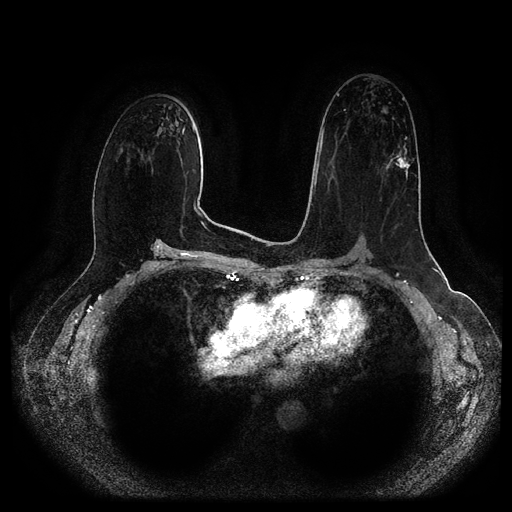
Breast MRI (dynamic contrast-enhanced, multi-phase), one axial slice; position 60 of 116 along the scan axis; dynamic contrast-enhanced series, time point 2 of 5 at this slice position (early post-contrast); 1.5 T; TE 2.6 ms, TR 5.2 ms; 512 × 512 image matrix, field of view 380 × 380 mm. Female patient, age 57 years.
Structures marked on this image (semi-automatically segmented with operator editing):
- breast lesion (labelled 'tumour' in the annotation; benign lesions carry a separate 'benign' label): bounding box (x1, y1, x2, y2) in pixels: (389, 153, 413, 178)